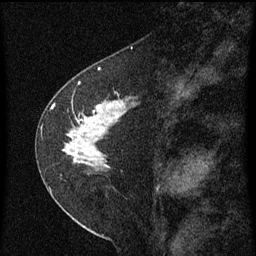
Breast MRI (dynamic contrast-enhanced), one sagittal slice; slice 32 of 60 in the series (ordered by position); dynamic contrast-enhanced series, image 2 of 3 at this slice position (ordered by acquisition); 1.5 T; TE 4.2 ms, TR 8 ms; 256 × 256 image matrix. Patient: female, 47 years.
Outlined on this slice (semi-automatic segmentation, software-assisted and operator-edited):
- analysis volume of interest (the breast-tissue region the enhancement analysis was run in; not a lesion): bounding box <44,84,141,199> (left, top, right, bottom; pixels)
- tumour enhancement mask (voxels above the 70 % enhancement threshold inside the analysis volume of interest): <62,100,125,161>